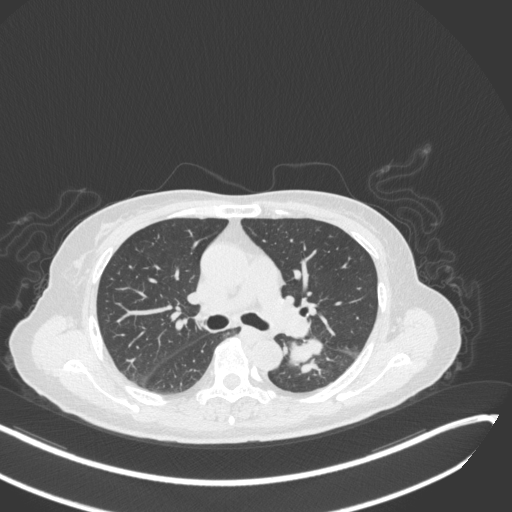
Chest CT, one axial slice; position 175 of 342 along the scan axis; 120 kVp; lung window (W 1500 / L -600 HU); 1 mm slice thickness; 512 × 512 image matrix, field of view 400 × 400 mm. Female patient, age 64 years. Case-level facts recorded for this patient, not image findings: clinical TNM (as recorded): T3 N1 M1.
Outlined on this slice (rectangle marked by the reading radiologist):
- lung tumour (recorded histology: small cell carcinoma): bounding box (x1, y1, x2, y2) in pixels: (286, 335, 326, 371)